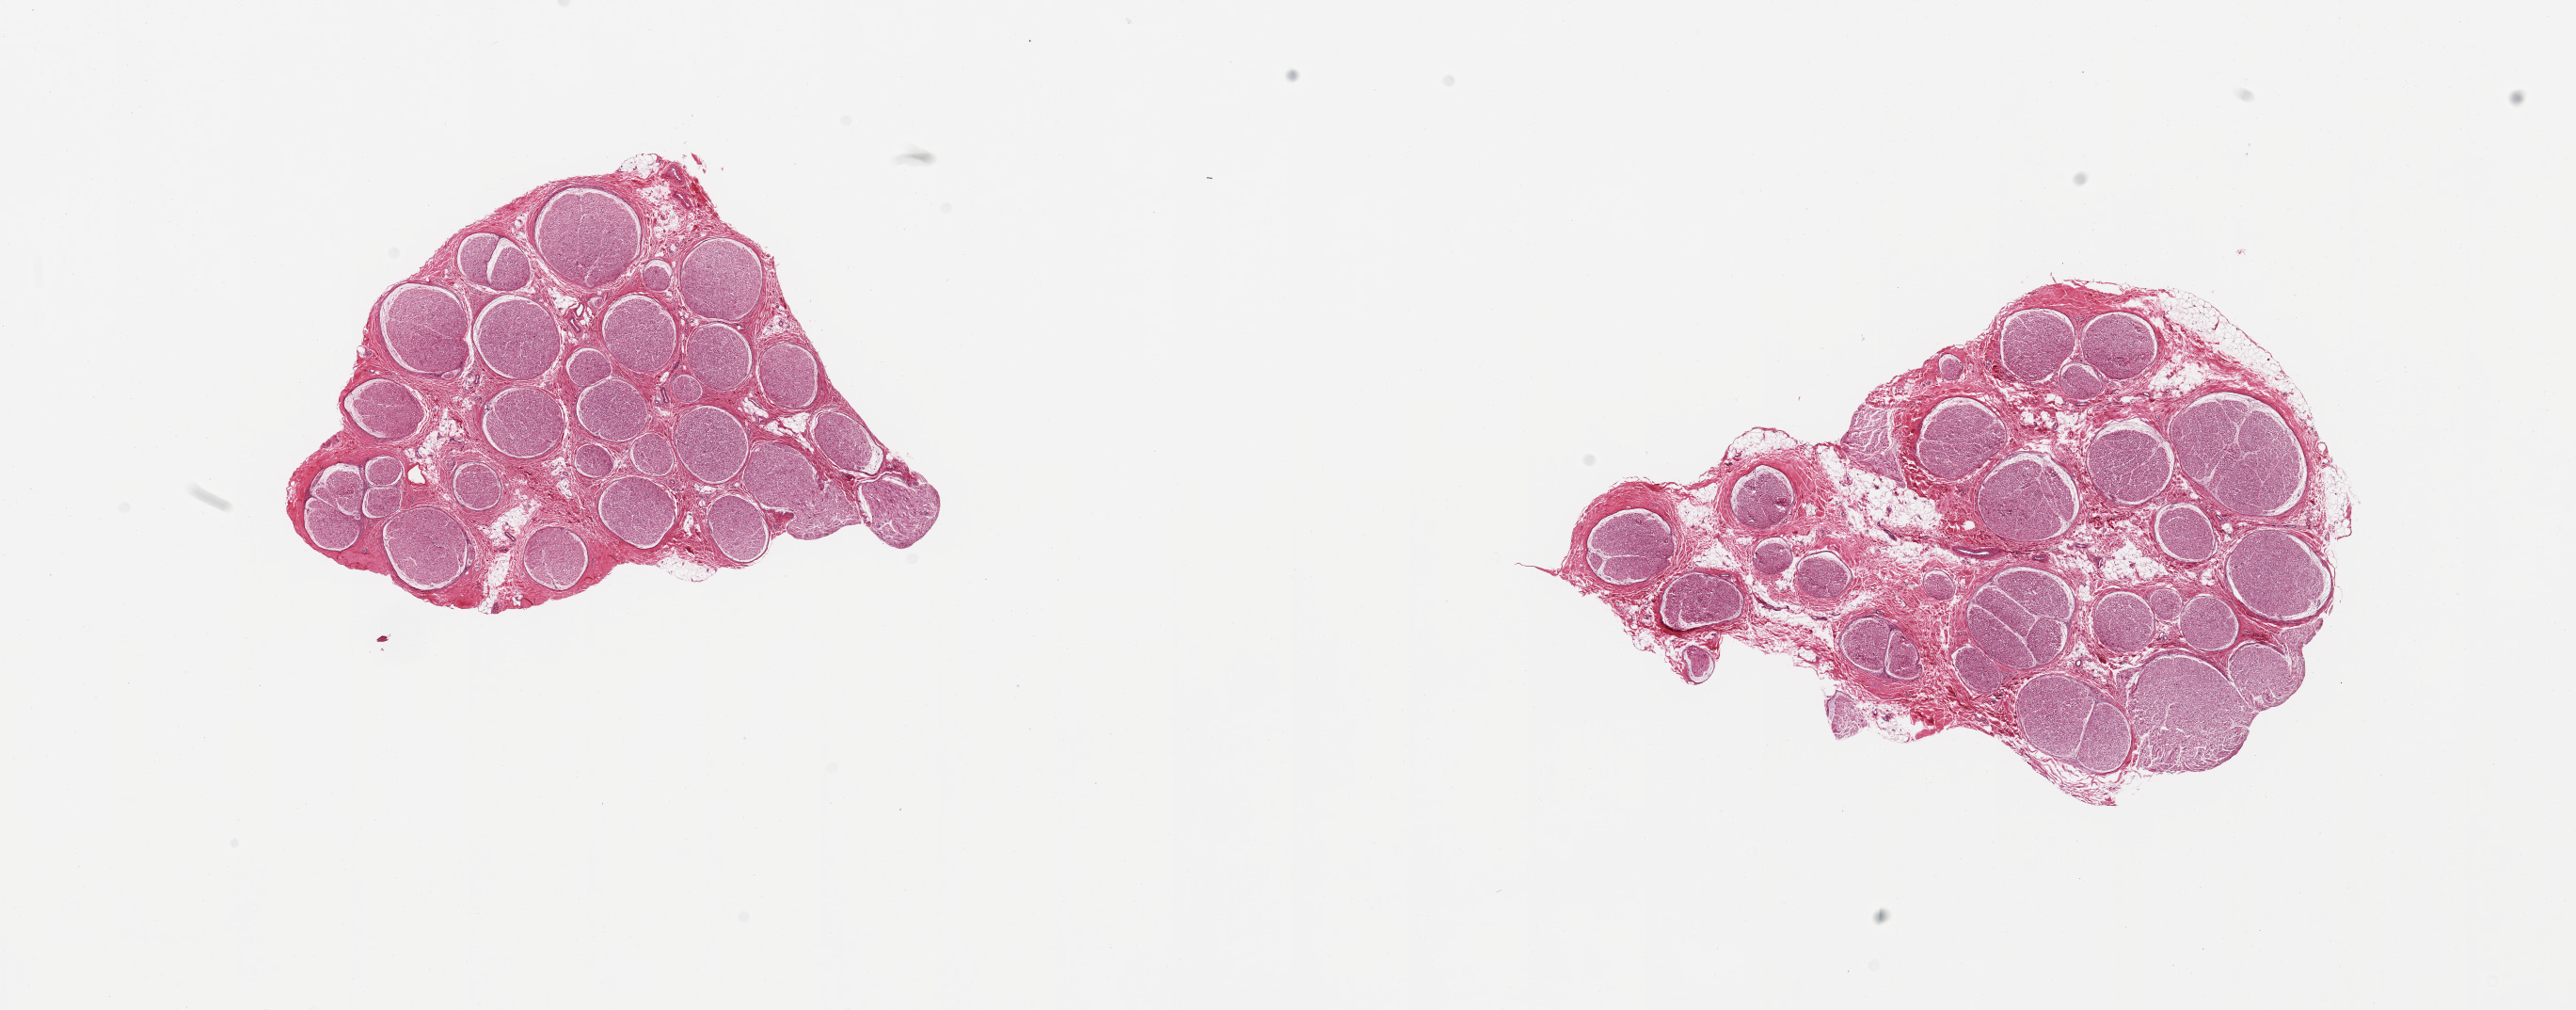
Hematoxylin and eosin (H&E) whole-slide image, brightfield, shown as a low-resolution overview of the whole scanned area (about 21.7 x 8.5 mm); PAXgene-fixed, paraffin-embedded tissue; section of tibial nerve (target tissue); donor tissue sample. Donor: male.
Review note (as recorded): 2 pieces; 1 piece has 10% internal fat.